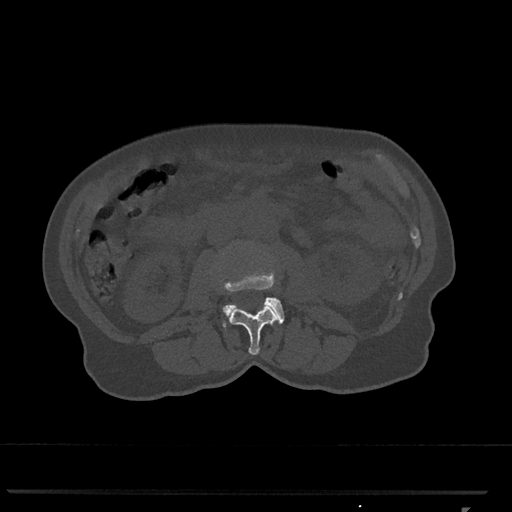
CT including the spine, one axial slice; position 306 of 793 along the scan axis; bone window (W 1800 / L 400 HU); 512 × 512 image matrix, field of view 380 × 380 mm. Female patient, age 62 years. Case-level facts recorded for this patient, not image findings: primary cancer: renal.
Structures marked on this image (semi-automatically segmented with operator editing):
- L2 vertebra: bounding box (x1, y1, x2, y2) in pixels: (228, 303, 278, 355)
- L3 vertebra: (223, 271, 285, 327)